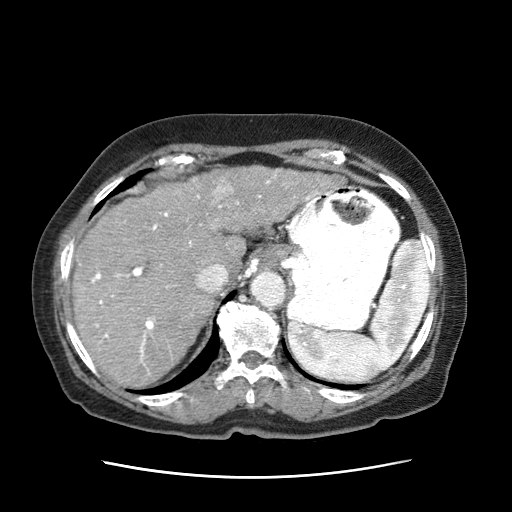
Contrast-enhanced abdominal CT (liver protocol), one axial slice. Slice 49 of 63 in the series (ordered by position). 120 kVp. Soft-tissue window (W 400 / L 40 HU). 2.5 mm slice thickness. 512 × 512 image matrix. Female patient, age 79 years. From the clinical record (not read from this slice): diagnosis: hepatocellular carcinoma (patient treated with transarterial chemoembolisation; whether this scan precedes or follows treatment is not stated here); TNM stage (as recorded): Stage-II; Child-Pugh class: B; tumour differentiation: well differentiated; tumour nodularity: multinodular.
Outlined on this slice (semi-automatic segmentation, software-assisted and operator-edited):
- abdominal aorta: box from (x=252, y=271) to (x=286, y=310) px
- liver parenchyma outside the tumour (the mass and vessels are separate outlines, so this box may not span the whole liver): (x=73, y=179)–(x=248, y=391)
- mass: (x=189, y=167)–(x=344, y=232)
- liver vessels: (x=91, y=195)–(x=296, y=363)